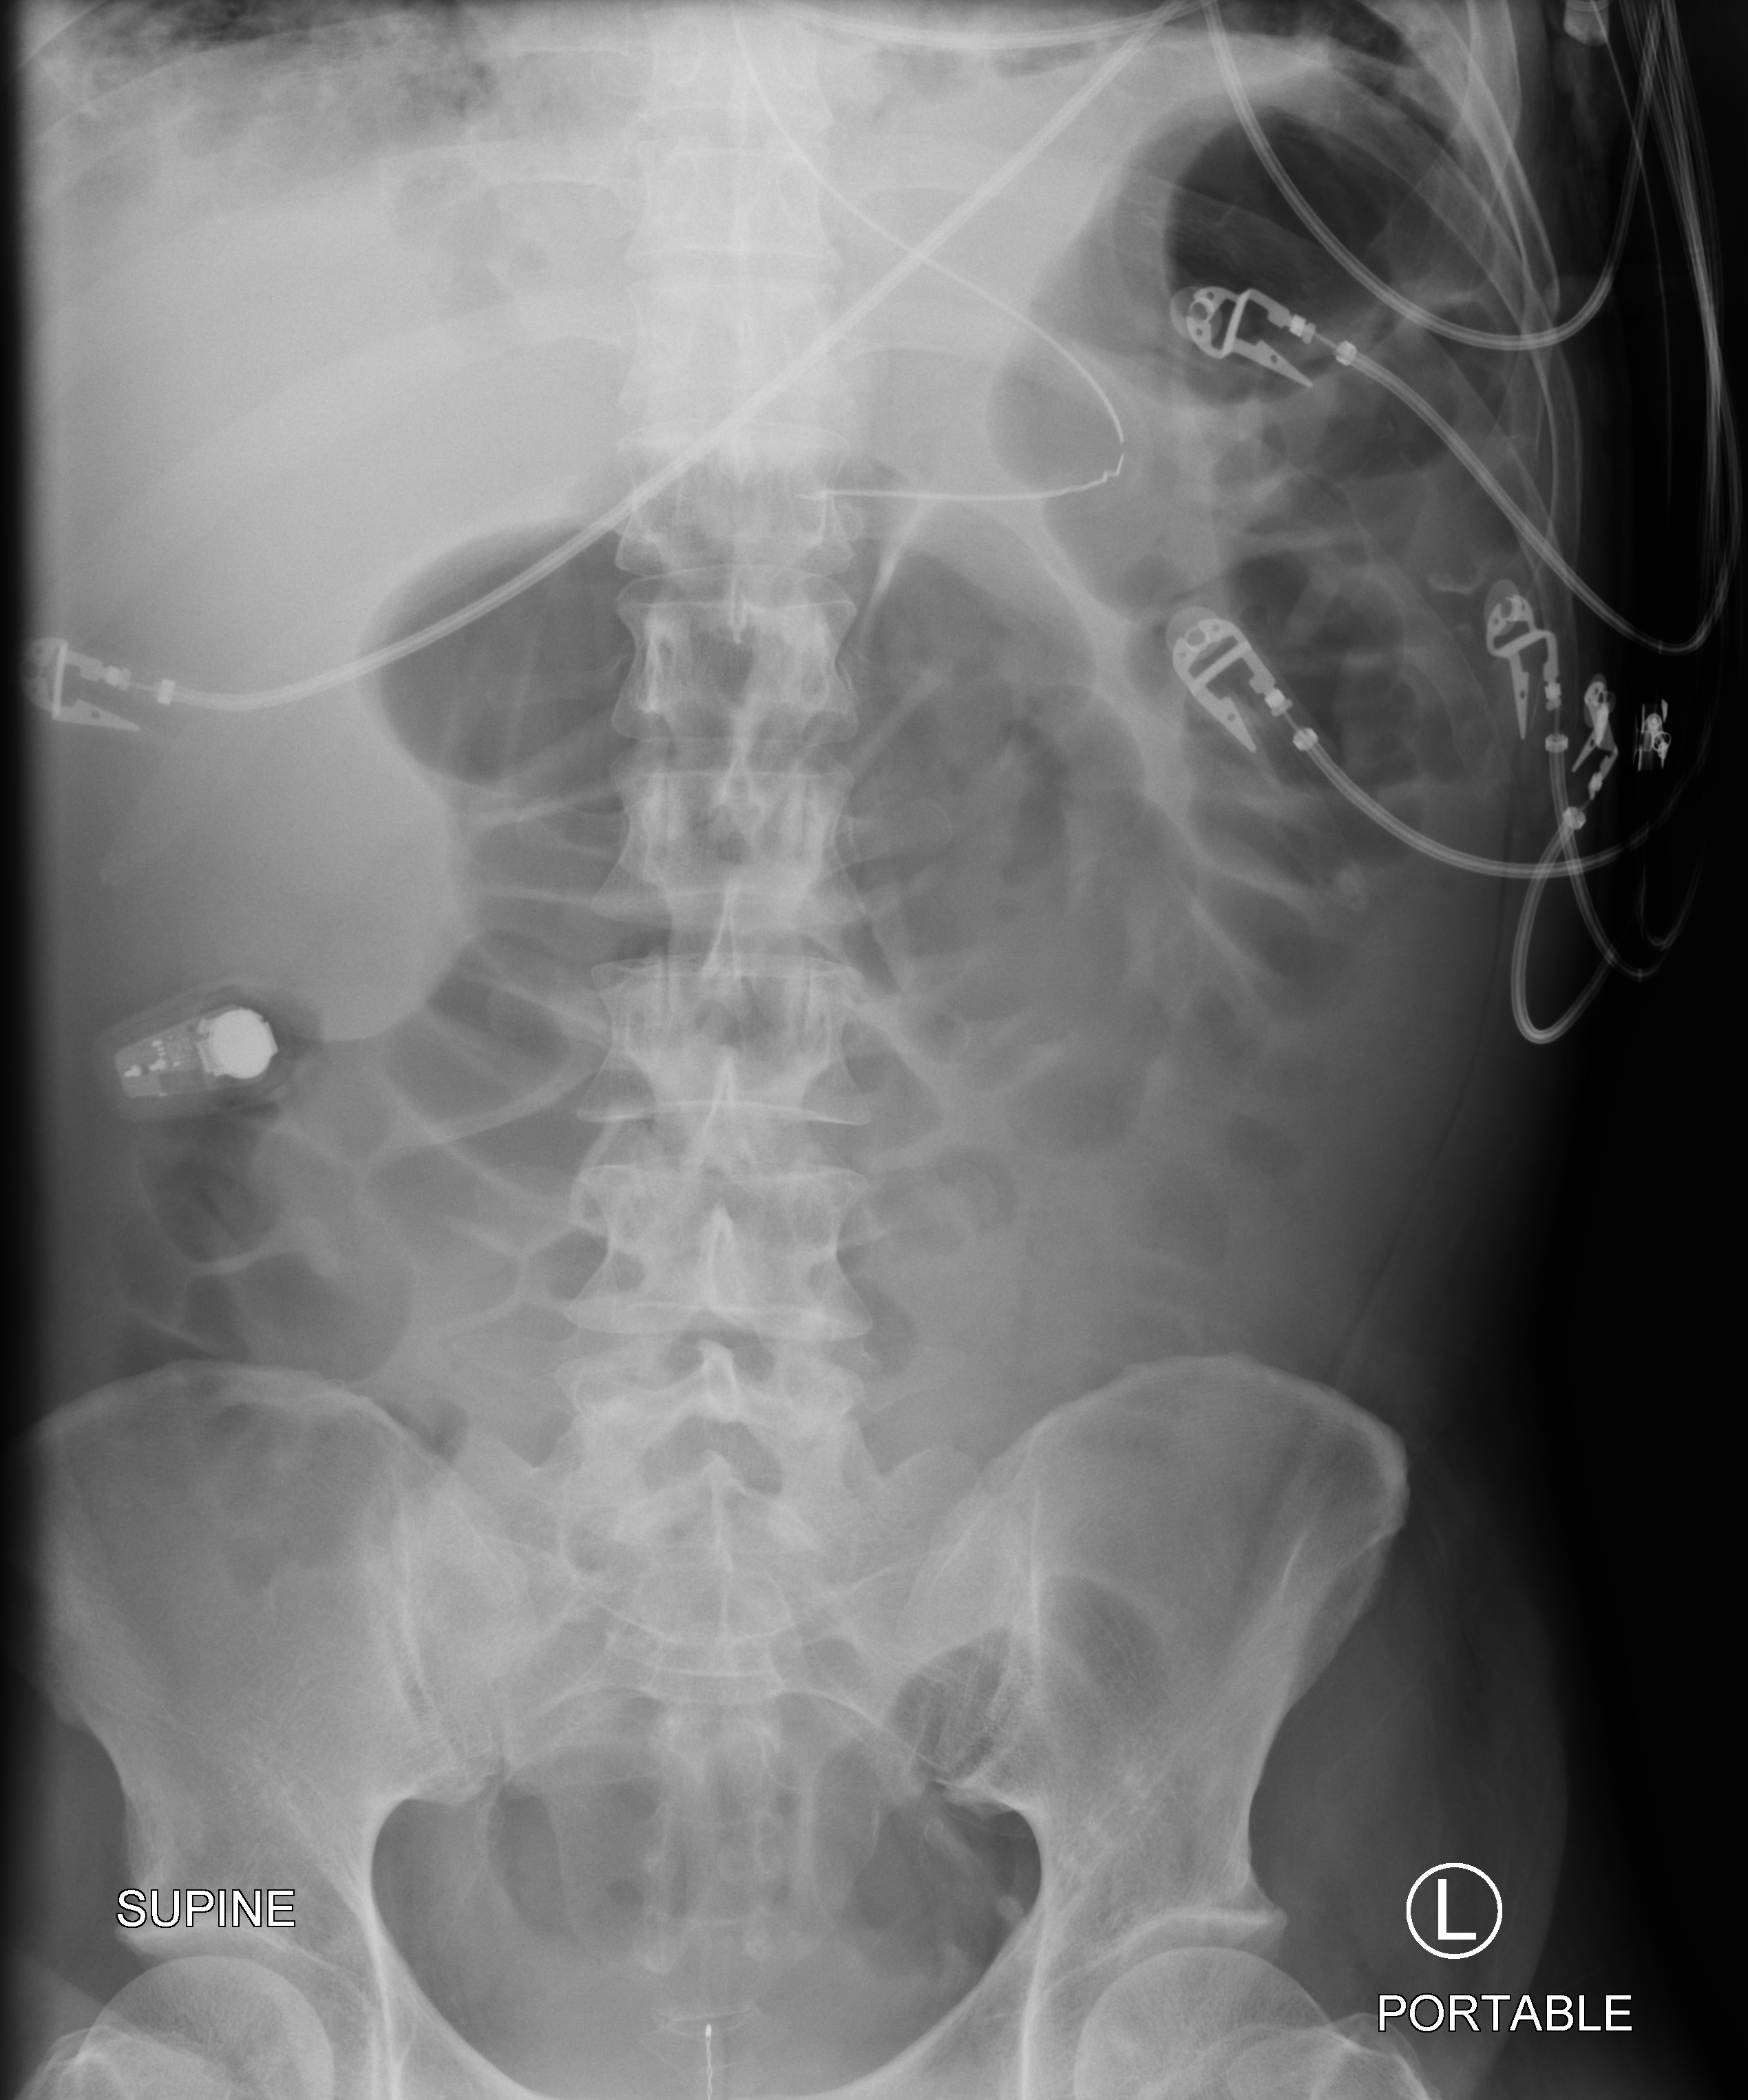
Portable abdomen radiograph, anteroposterior (AP) projection. Patient hospitalised with COVID-19; male, aged 18–59 years.
From the hospital-stay record, not from the radiograph (when in the stay this image was taken is not recorded): mechanically ventilated during this hospital stay: yes.